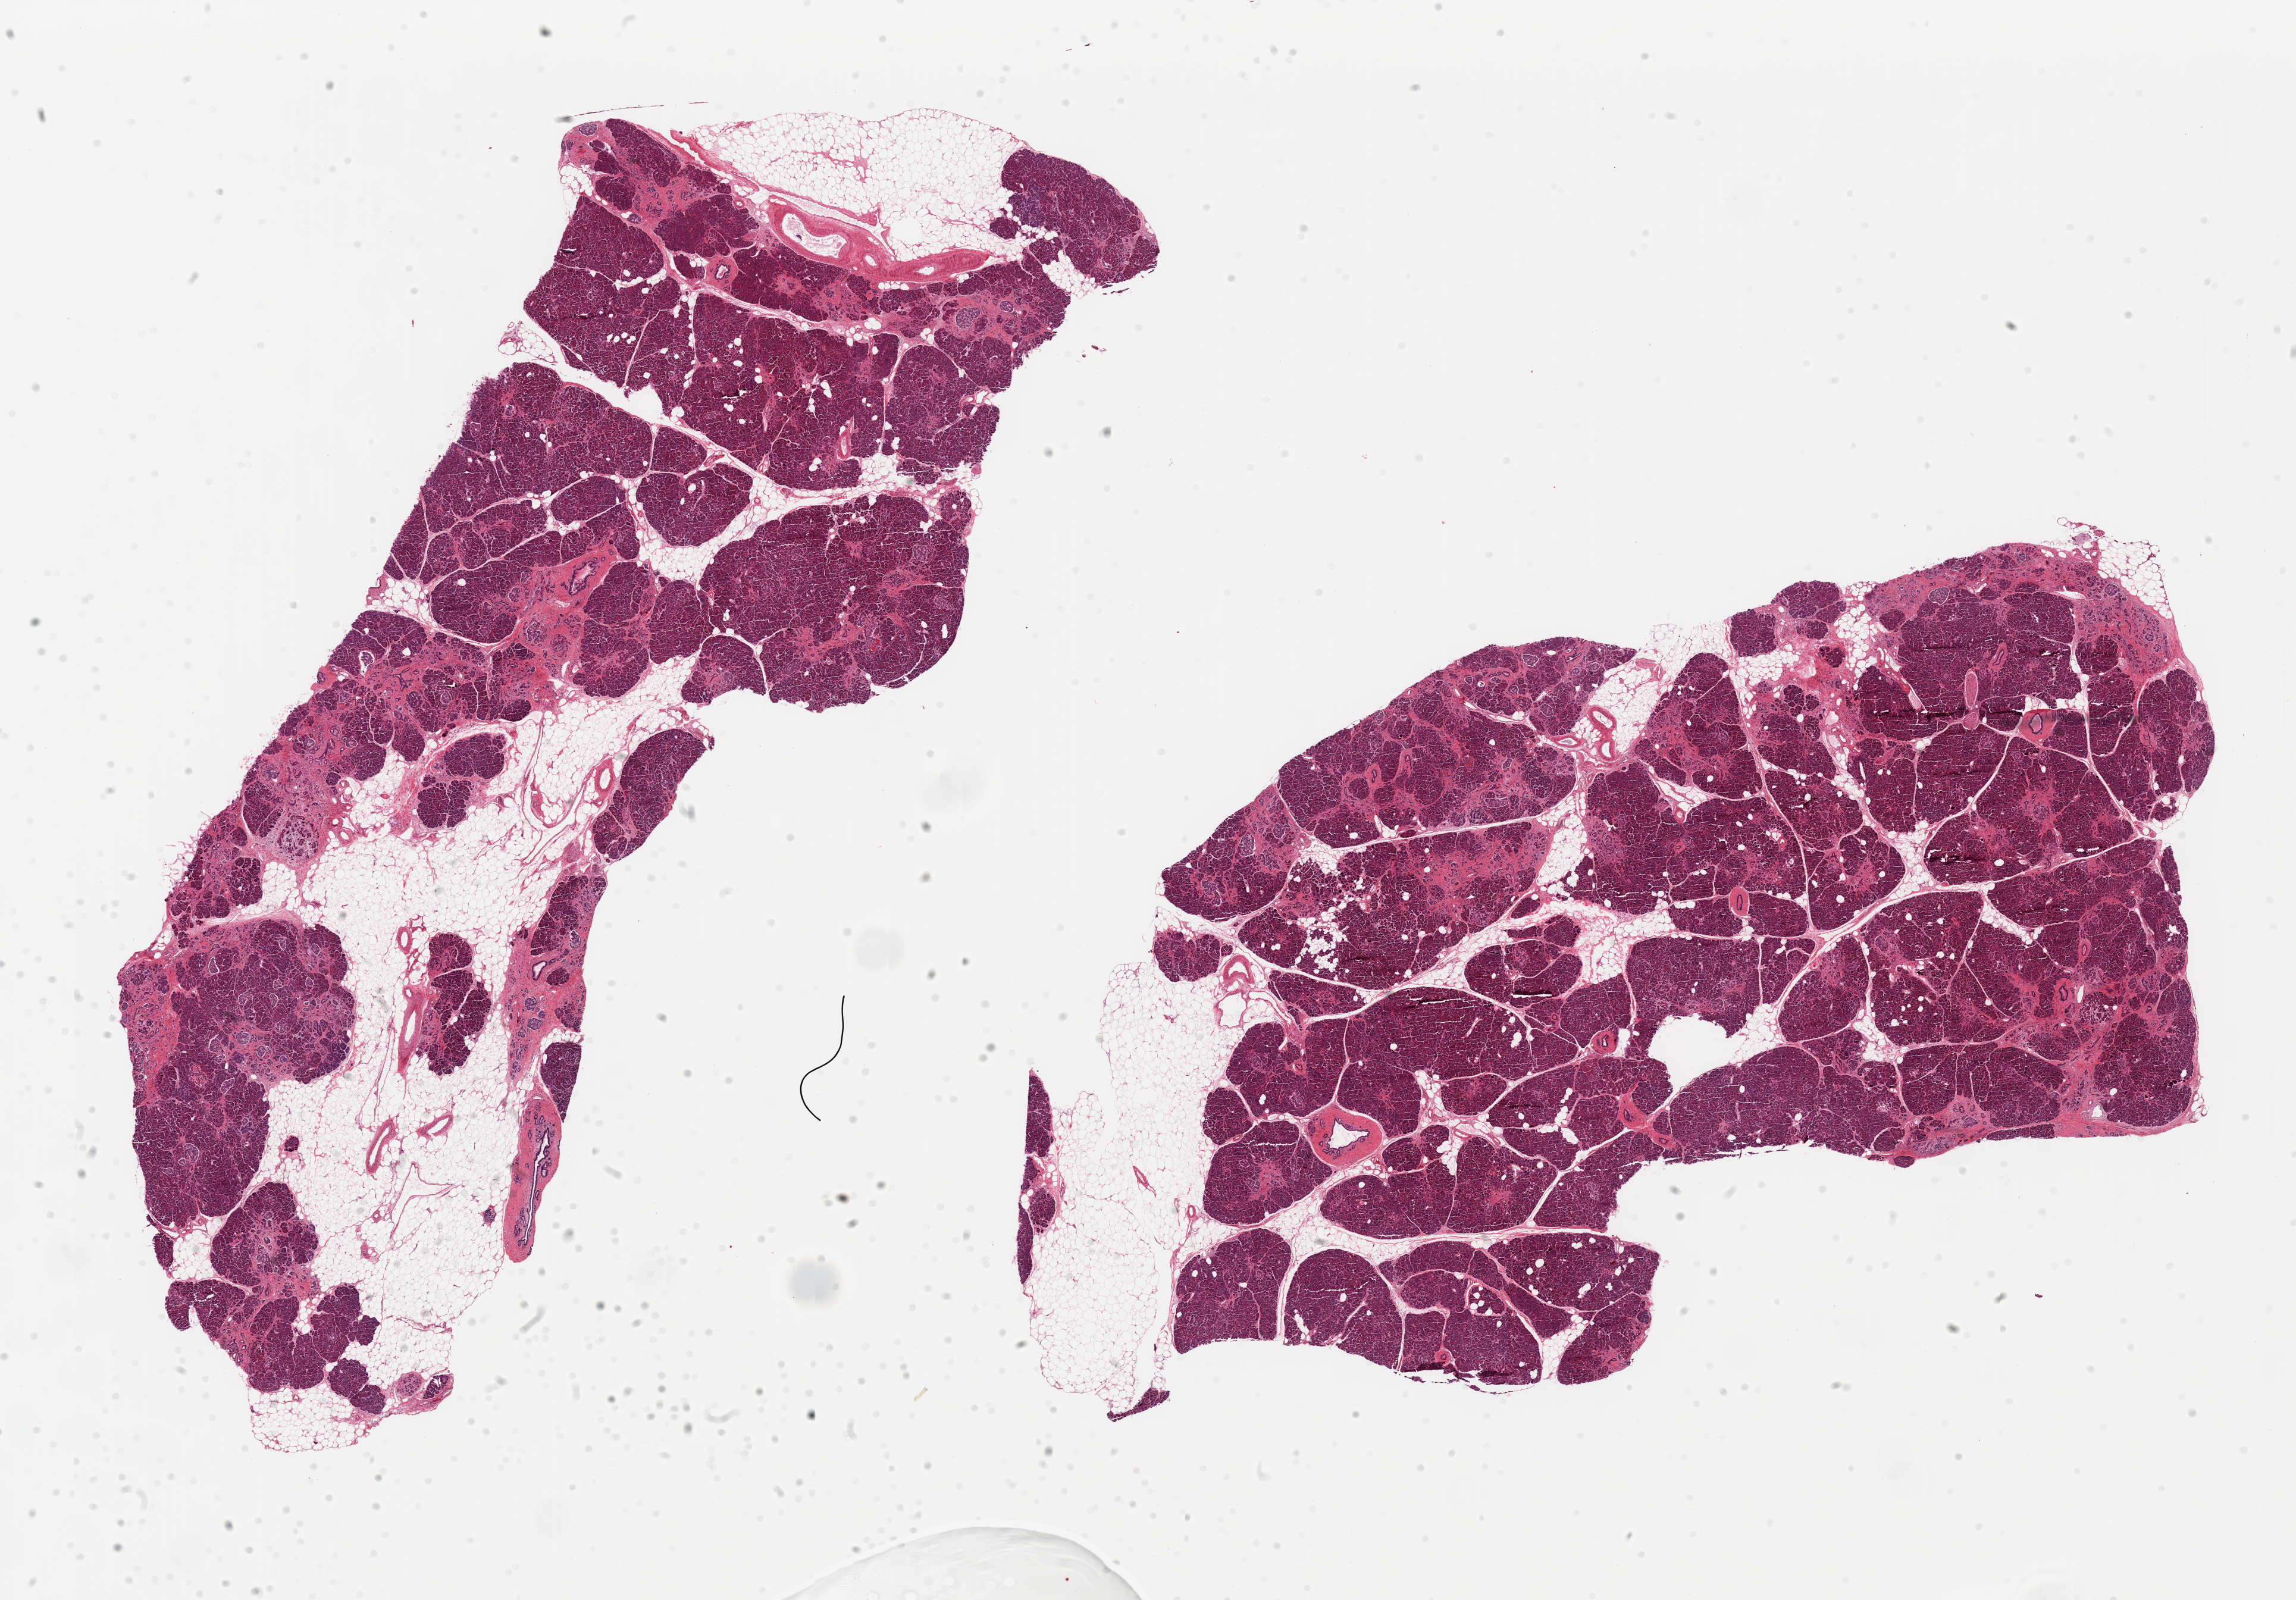
Digitized H&E-stained section, low-resolution overview of the scanned area, about 30.5 x 21.3 mm (from a 20x scan), PAXgene-fixed, paraffin-embedded tissue, target tissue: pancreas, donor tissue sample. Male donor.
Review note (as recorded): 2 pieces; 30% interstitial fibrosis and exocrine atrophy; 20 and 30% internal and external fat.